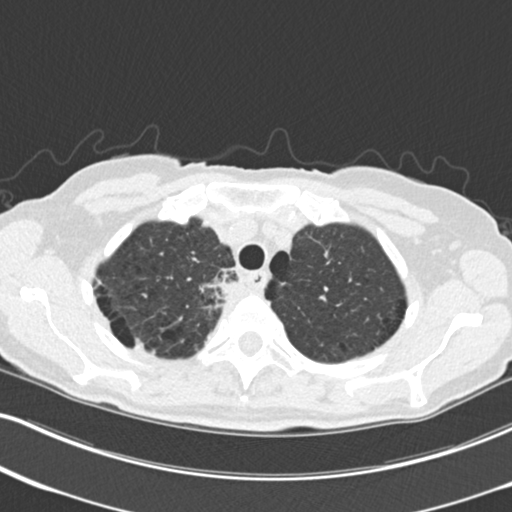
Low-dose screening chest CT, one axial slice; position 185 of 226 along the scan axis; lung window (W 1500 / L -600 HU); 2 mm slice thickness; 512 × 512 image matrix, field of view 322 × 322 mm.
Annotated regions visible in this slice (expert manual segmentation):
- lesion 1 (tumor, mediastinum): bounding box [x1, y1, x2, y2] px = [207, 268, 237, 301]